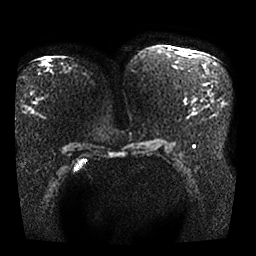
Breast MRI, one axial slice; position 9 of 25 along the scan axis; diffusion-weighted series; image 2 of 4 stored at this slice position (different b-values; order by instance number); 1.5 T; 4 mm slice thickness; 256 × 256 image matrix. Female patient.
Outlined on this slice (outlined manually by an expert reader):
- tumour on diffusion-weighted imaging: bounding box <197,107,205,113> (left, top, right, bottom; pixels)